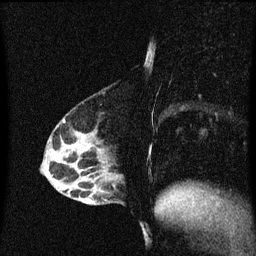
Breast MRI (dynamic contrast-enhanced), one sagittal slice. Slice 19 of 60 in the series (ordered by position). Dynamic contrast-enhanced series, image 2 of 3 at this slice position (ordered by acquisition). 1.5 T. TE 4.2 ms, TR 8.4 ms. 2 mm slice thickness. 256 × 256 image matrix, field of view 200 × 200 mm. Female patient, age 40 years.
Structures marked on this image (semi-automatically segmented with operator editing):
- analysis volume of interest (the breast-tissue region the enhancement analysis was run in; not a lesion): box from (x=82, y=172) to (x=122, y=205) px
- tumour enhancement mask (voxels above the 70 % enhancement threshold inside the analysis volume of interest): (x=82, y=200)–(x=90, y=205)